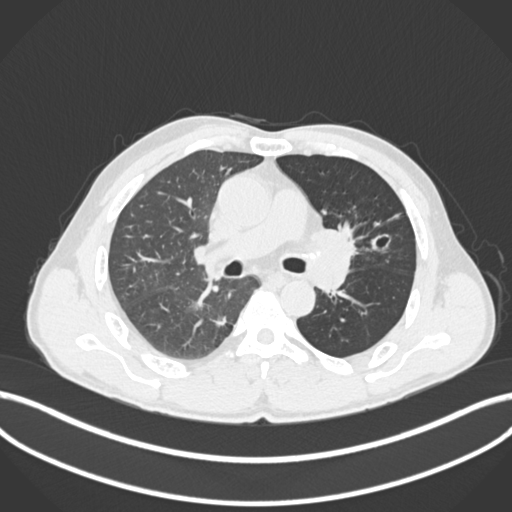
Chest CT, one axial slice; position 112 of 255 along the scan axis; 120 kVp; lung window (W 1500 / L -600 HU); 1 mm slice thickness; 512 × 512 image matrix, field of view 400 × 400 mm. Patient: male, 57 years. Case-level facts recorded for this patient, not image findings: clinical TNM (as recorded): T2b N0 M0.
Annotated regions visible in this slice (bounding box drawn by a radiologist):
- lung tumour (recorded histology: squamous cell carcinoma): bounding box [x1, y1, x2, y2] px = [312, 220, 362, 261]